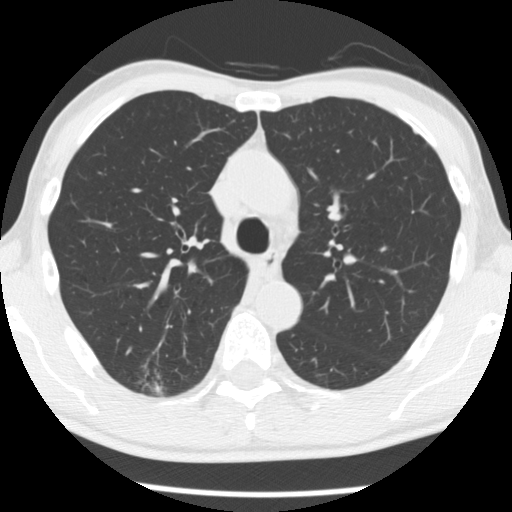
Chest CT (low-dose screening protocol), one axial image; first (baseline) screen; lung window (W 1500 / L -600 HU); 2.5 mm slice thickness; standard (soft-tissue) reconstruction kernel (STANDARD); 512 × 512 image matrix, field of view 320 × 320 mm. Male participant, aged 66 years at enrolment.
Expert reader's lesion annotation, bounding box <130,356,192,405> (left, top, right, bottom; pixels). The screening reader recorded 4 non-calcified nodules or masses ≥4 mm on this exam; which of them this box marks is not recorded. Later outcome: lung cancer diagnosed 503 days after this screen — adenocarcinoma, NOS, right upper lobe, undifferentiated (G4), stage IA (AJCC 6th edition), 20 mm at pathology.